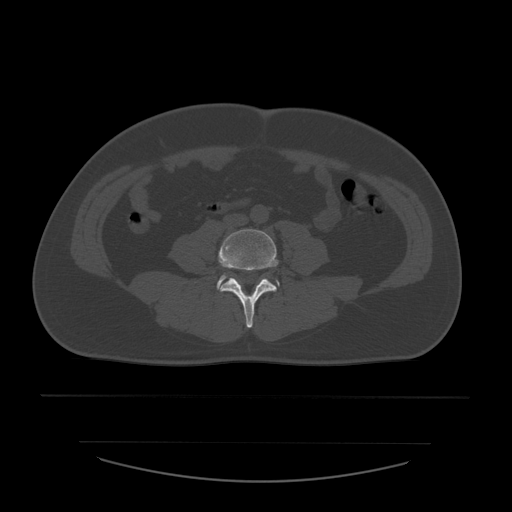
CT including the spine, one axial slice. Position 140 of 532 along the scan axis. Bone window (W 1800 / L 400 HU). 1.25 mm slice thickness. 512 × 512 image matrix, field of view 441 × 441 mm. Patient age 44 years. From the clinical record (not read from this slice): primary cancer: soft tissue sarcoma.
Structures marked on this image (semi-automatic segmentation, software-assisted and operator-edited):
- L4 vertebra: bounding box <219,229,278,328> (left, top, right, bottom; pixels)
- L5 vertebra: <217,275,280,290>